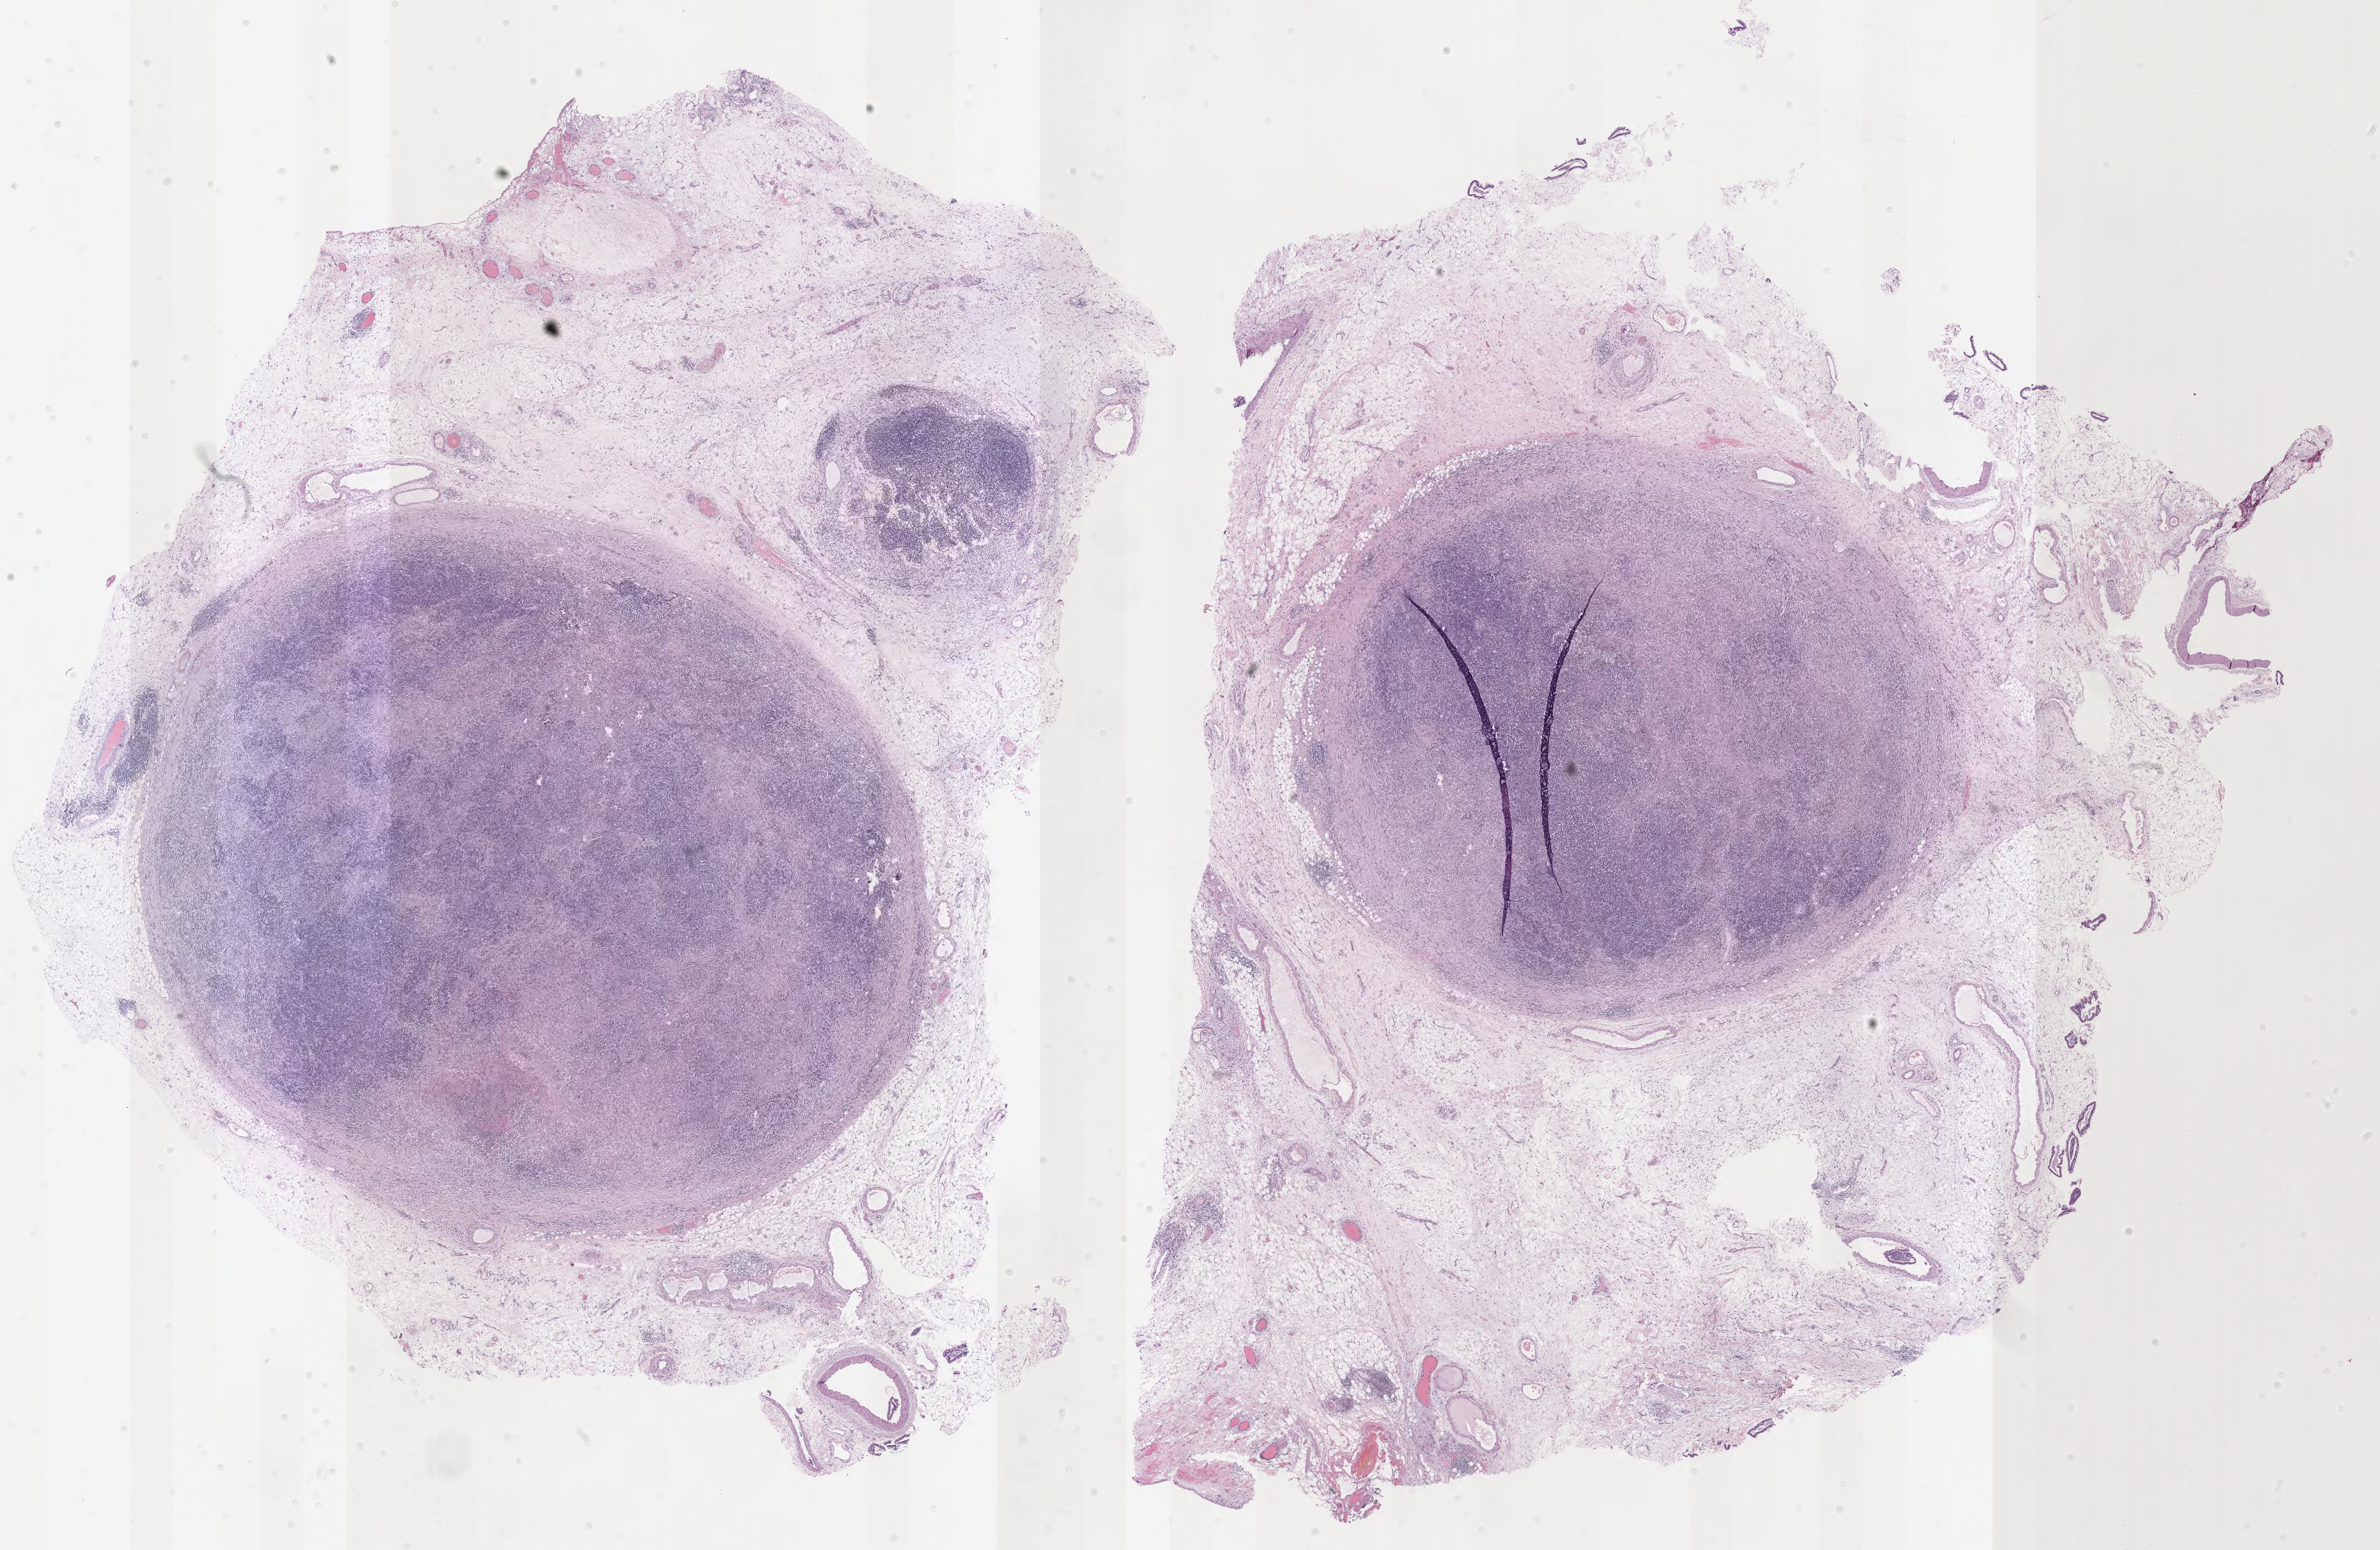
Digitized H&E-stained section — low-resolution overview of the scanned area, about 27.7 x 18.0 mm. Tumor tissue. Patient: female, 44 years old.
Histologic diagnosis: Burkitt lymphoma, NOS.